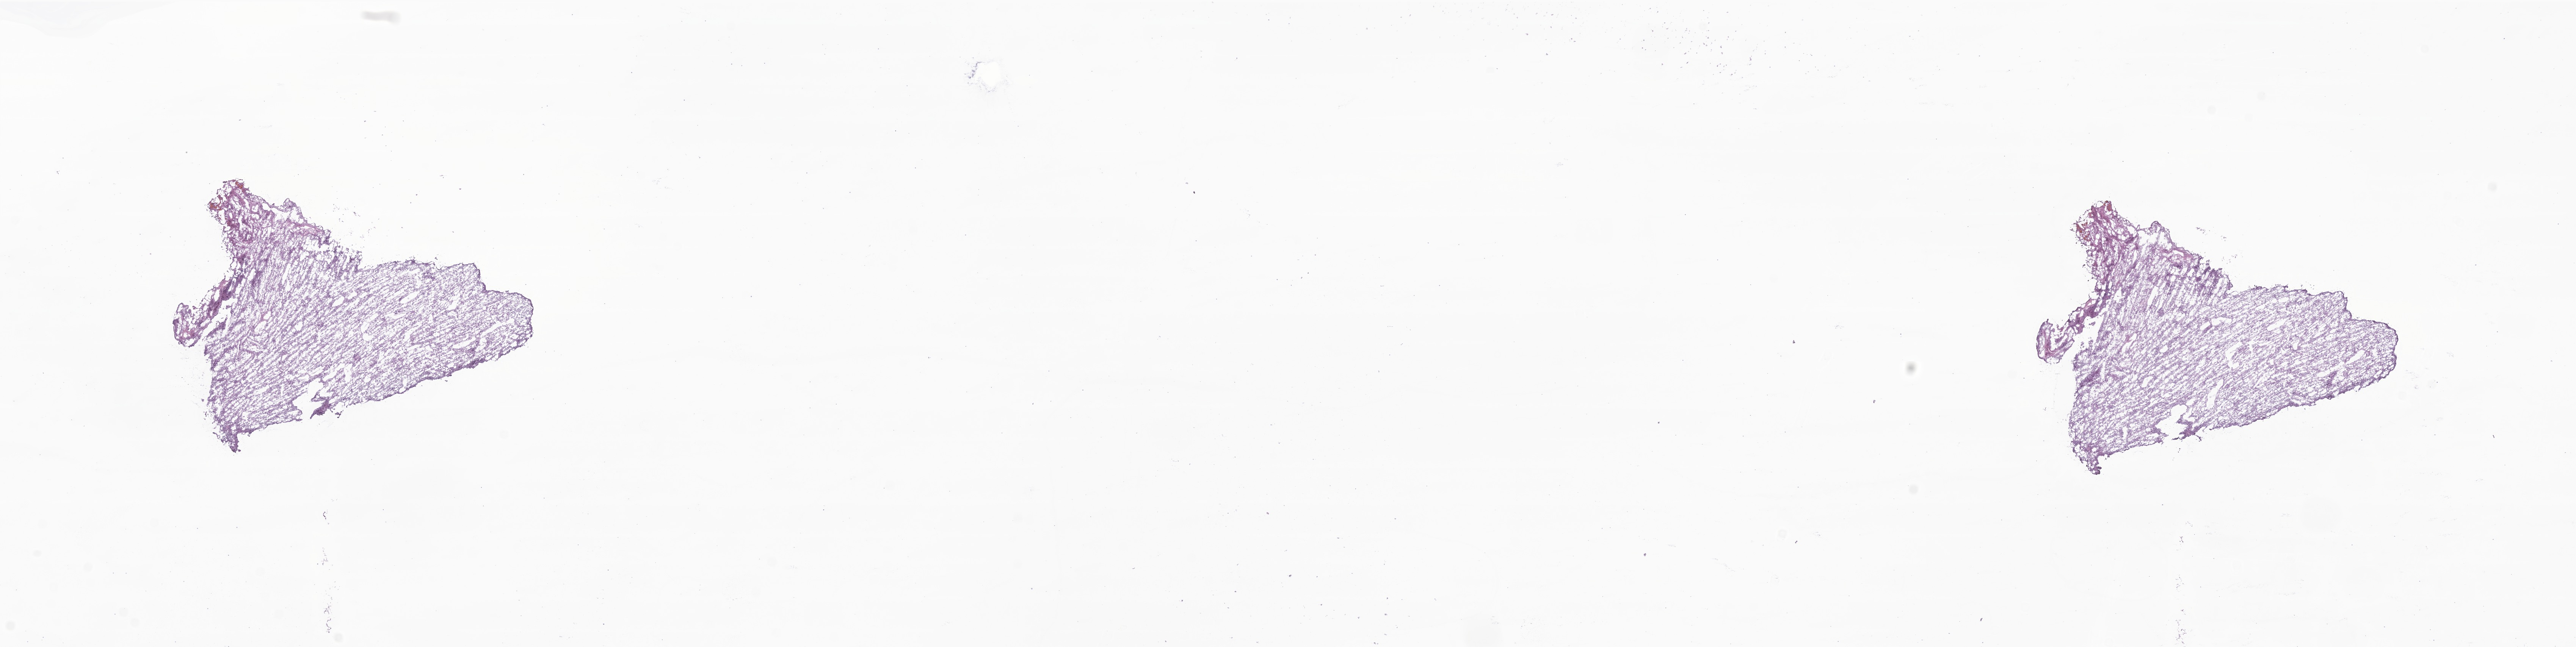
Digitized H&E-stained section of tumor tissue from the pelvis, a low-resolution overview of the entire scanned area, about 28.7 x 7.2 mm; frozen section (OCT-embedded). Patient: male, age 176 months (14 years 8 months).
* recorded diagnosis: Rhabdomyosarcoma, NOS